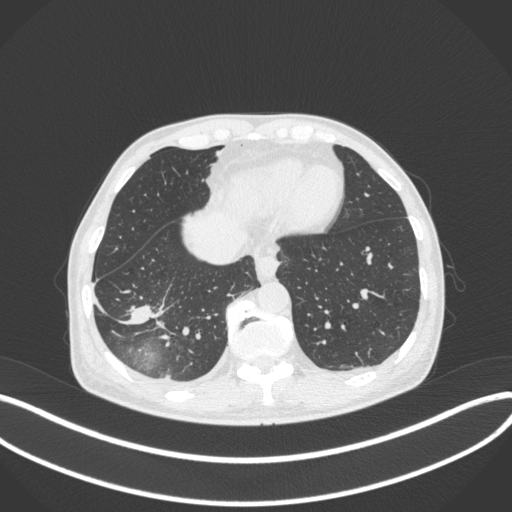
Chest CT, one axial slice; position 95 of 385 along the scan axis; reconstruction kernel B31f; lung window (W 1500 / L -600 HU); 1 mm slice thickness; 512 × 512 image matrix, field of view 400 × 400 mm. Patient: male, 64 years. Case-level facts recorded for this patient, not image findings: clinical TNM (as recorded): T3 N0 M0; histopathological grade: G2-3.
Structures marked on this image (rectangle marked by the reading radiologist):
- lung tumour (recorded histology: adenocarcinoma): bounding box (x1, y1, x2, y2) in pixels: (126, 293, 161, 327)